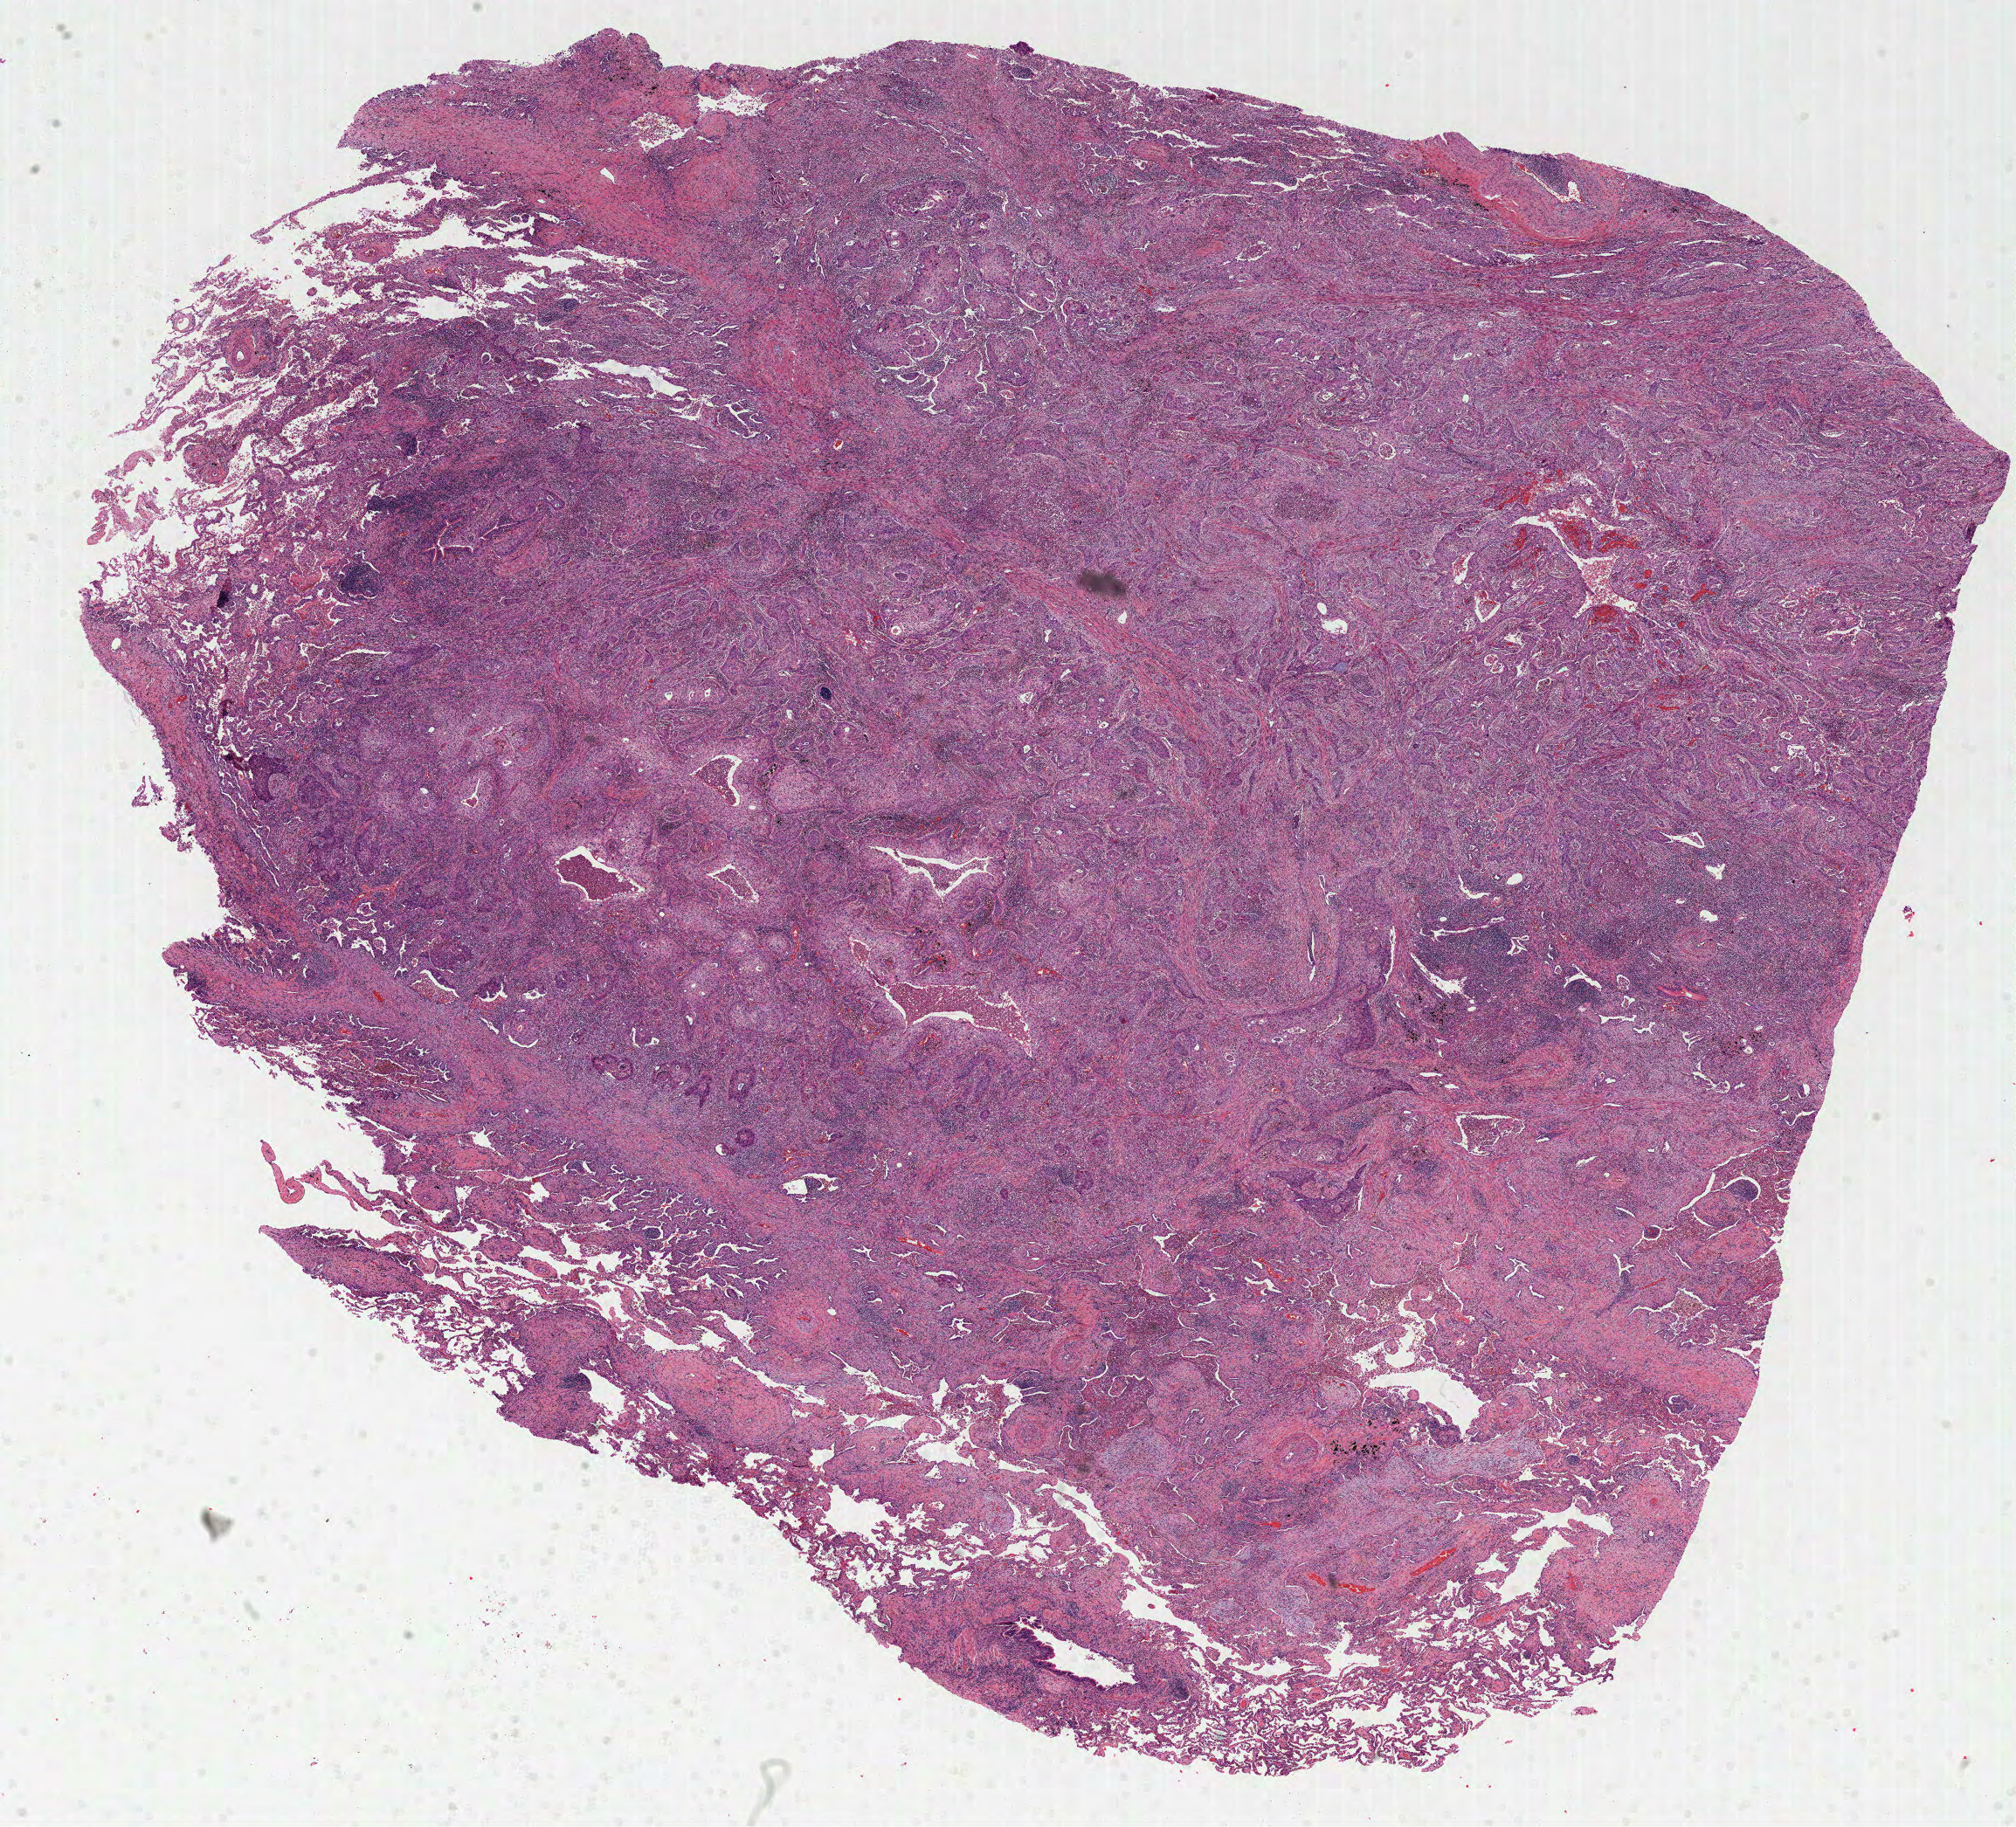
Digitized Hematoxylin and eosin (H&E) stained tissue section (whole slide) — shown as a low-resolution overview of the whole scanned area (about 18.6 x 16.9 mm, from a 40x scan). Formalin-fixed paraffin-embedded (FFPE) diagnostic section. Lung, primary tumour sample. Patient: male, age at initial diagnosis 74 years.
AJCC pathologic stage: IA (7th edition). Pathologic diagnosis: Squamous cell carcinoma, NOS (upper lobe, lung). Laterality: left. TNM: T1b N0 MX.